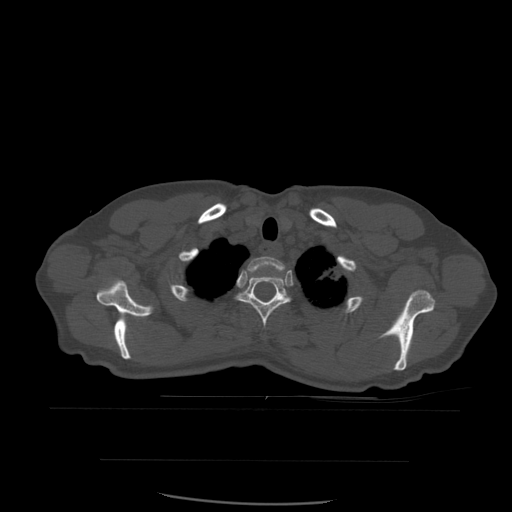
CT including the spine, one axial slice; position 458 of 574 along the scan axis; bone window (W 1800 / L 400 HU); 512 × 512 image matrix, field of view 392 × 392 mm. Patient age 48 years. From the clinical record (not read from this slice): primary cancer: lung.
Structures marked on this image (semi-automatic segmentation, software-assisted and operator-edited):
- T1 vertebra: box from (x=248, y=257) to (x=285, y=272) px
- T2 vertebra: (x=236, y=266)–(x=291, y=329)